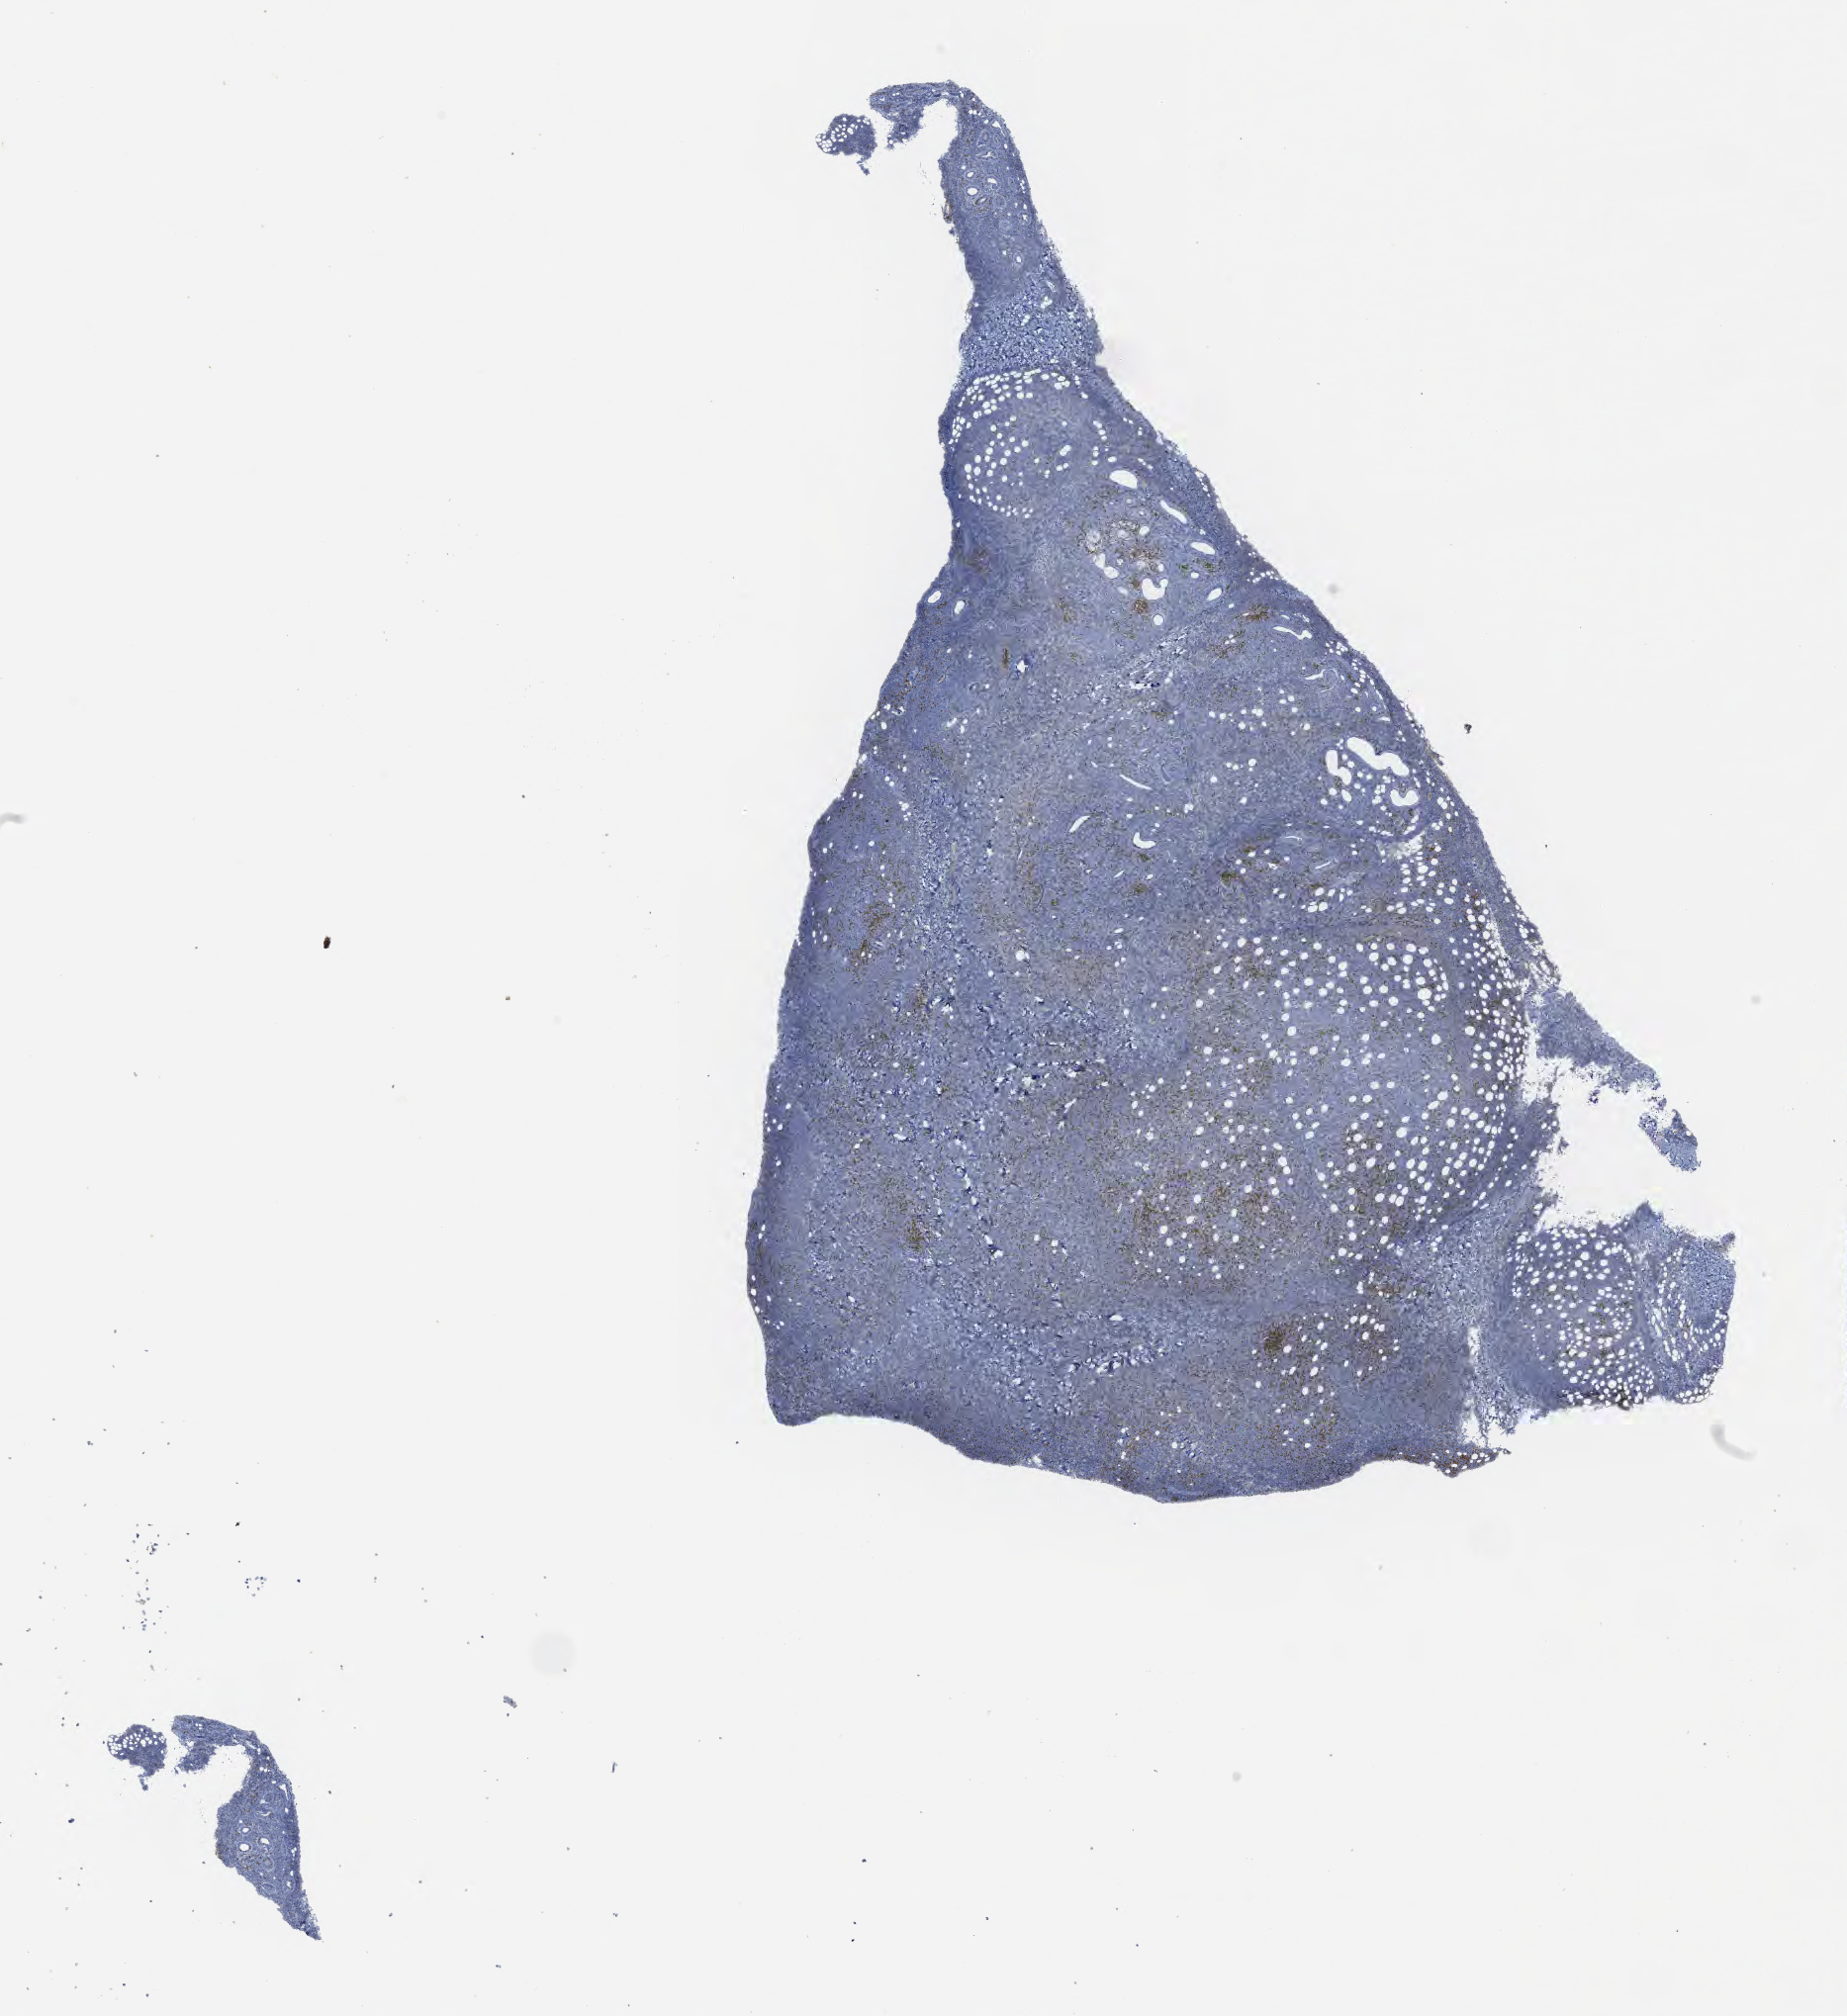
Whole-slide image, immunohistochemical stain for CD3 — whole scanned area (about 15.1 x 16.5 mm) shown as a low-resolution overview. Tumor tissue. Patient male; aged 46.
Histologic diagnosis: Burkitt lymphoma, NOS.